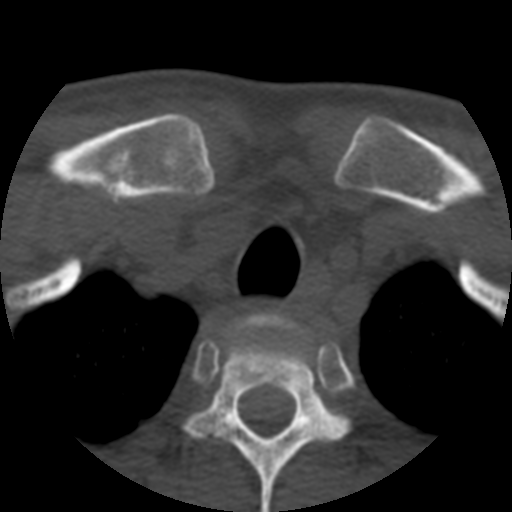
CT including the spine, one axial slice. Slice 433 of 508 in the series (ordered by position). 120 kVp. Bone window (W 1800 / L 400 HU). 512 × 512 image matrix. Patient age 57 years. From the clinical record (not read from this slice): primary cancer: prostate.
Outlined on this slice (semi-automatically segmented with operator editing):
- T1 vertebra: bounding box <302,332,311,347> (left, top, right, bottom; pixels)
- T2 vertebra: <181,317,350,512>